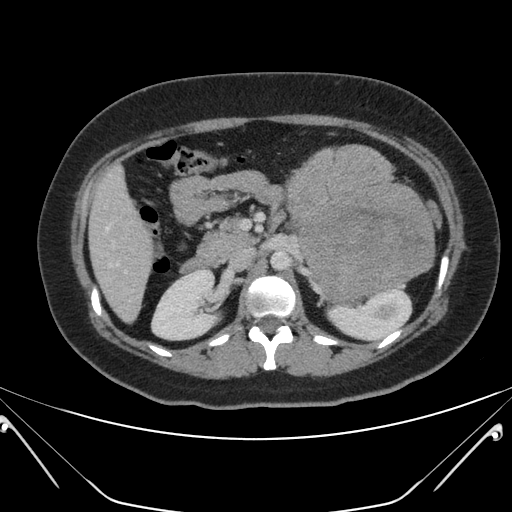
Contrast-enhanced abdominal CT, one axial slice; slice 116 of 168 in the series (ordered by position); 120 kVp; soft-tissue window (W 400 / L 40 HU); 3 mm slice thickness; 512 × 512 image matrix, field of view 394 × 394 mm. Patient: female, 26 years. From the clinical record (not read from this slice): diagnosis: adrenocortical carcinoma; tumour side: left adrenal; tumour size at pathology: 28 cm; Ki-67 index: 20 %.
Annotated regions visible in this slice (semi-automatic segmentation, software-assisted and operator-edited):
- mass: bounding box (x1, y1, x2, y2) in pixels: (287, 141, 437, 302)